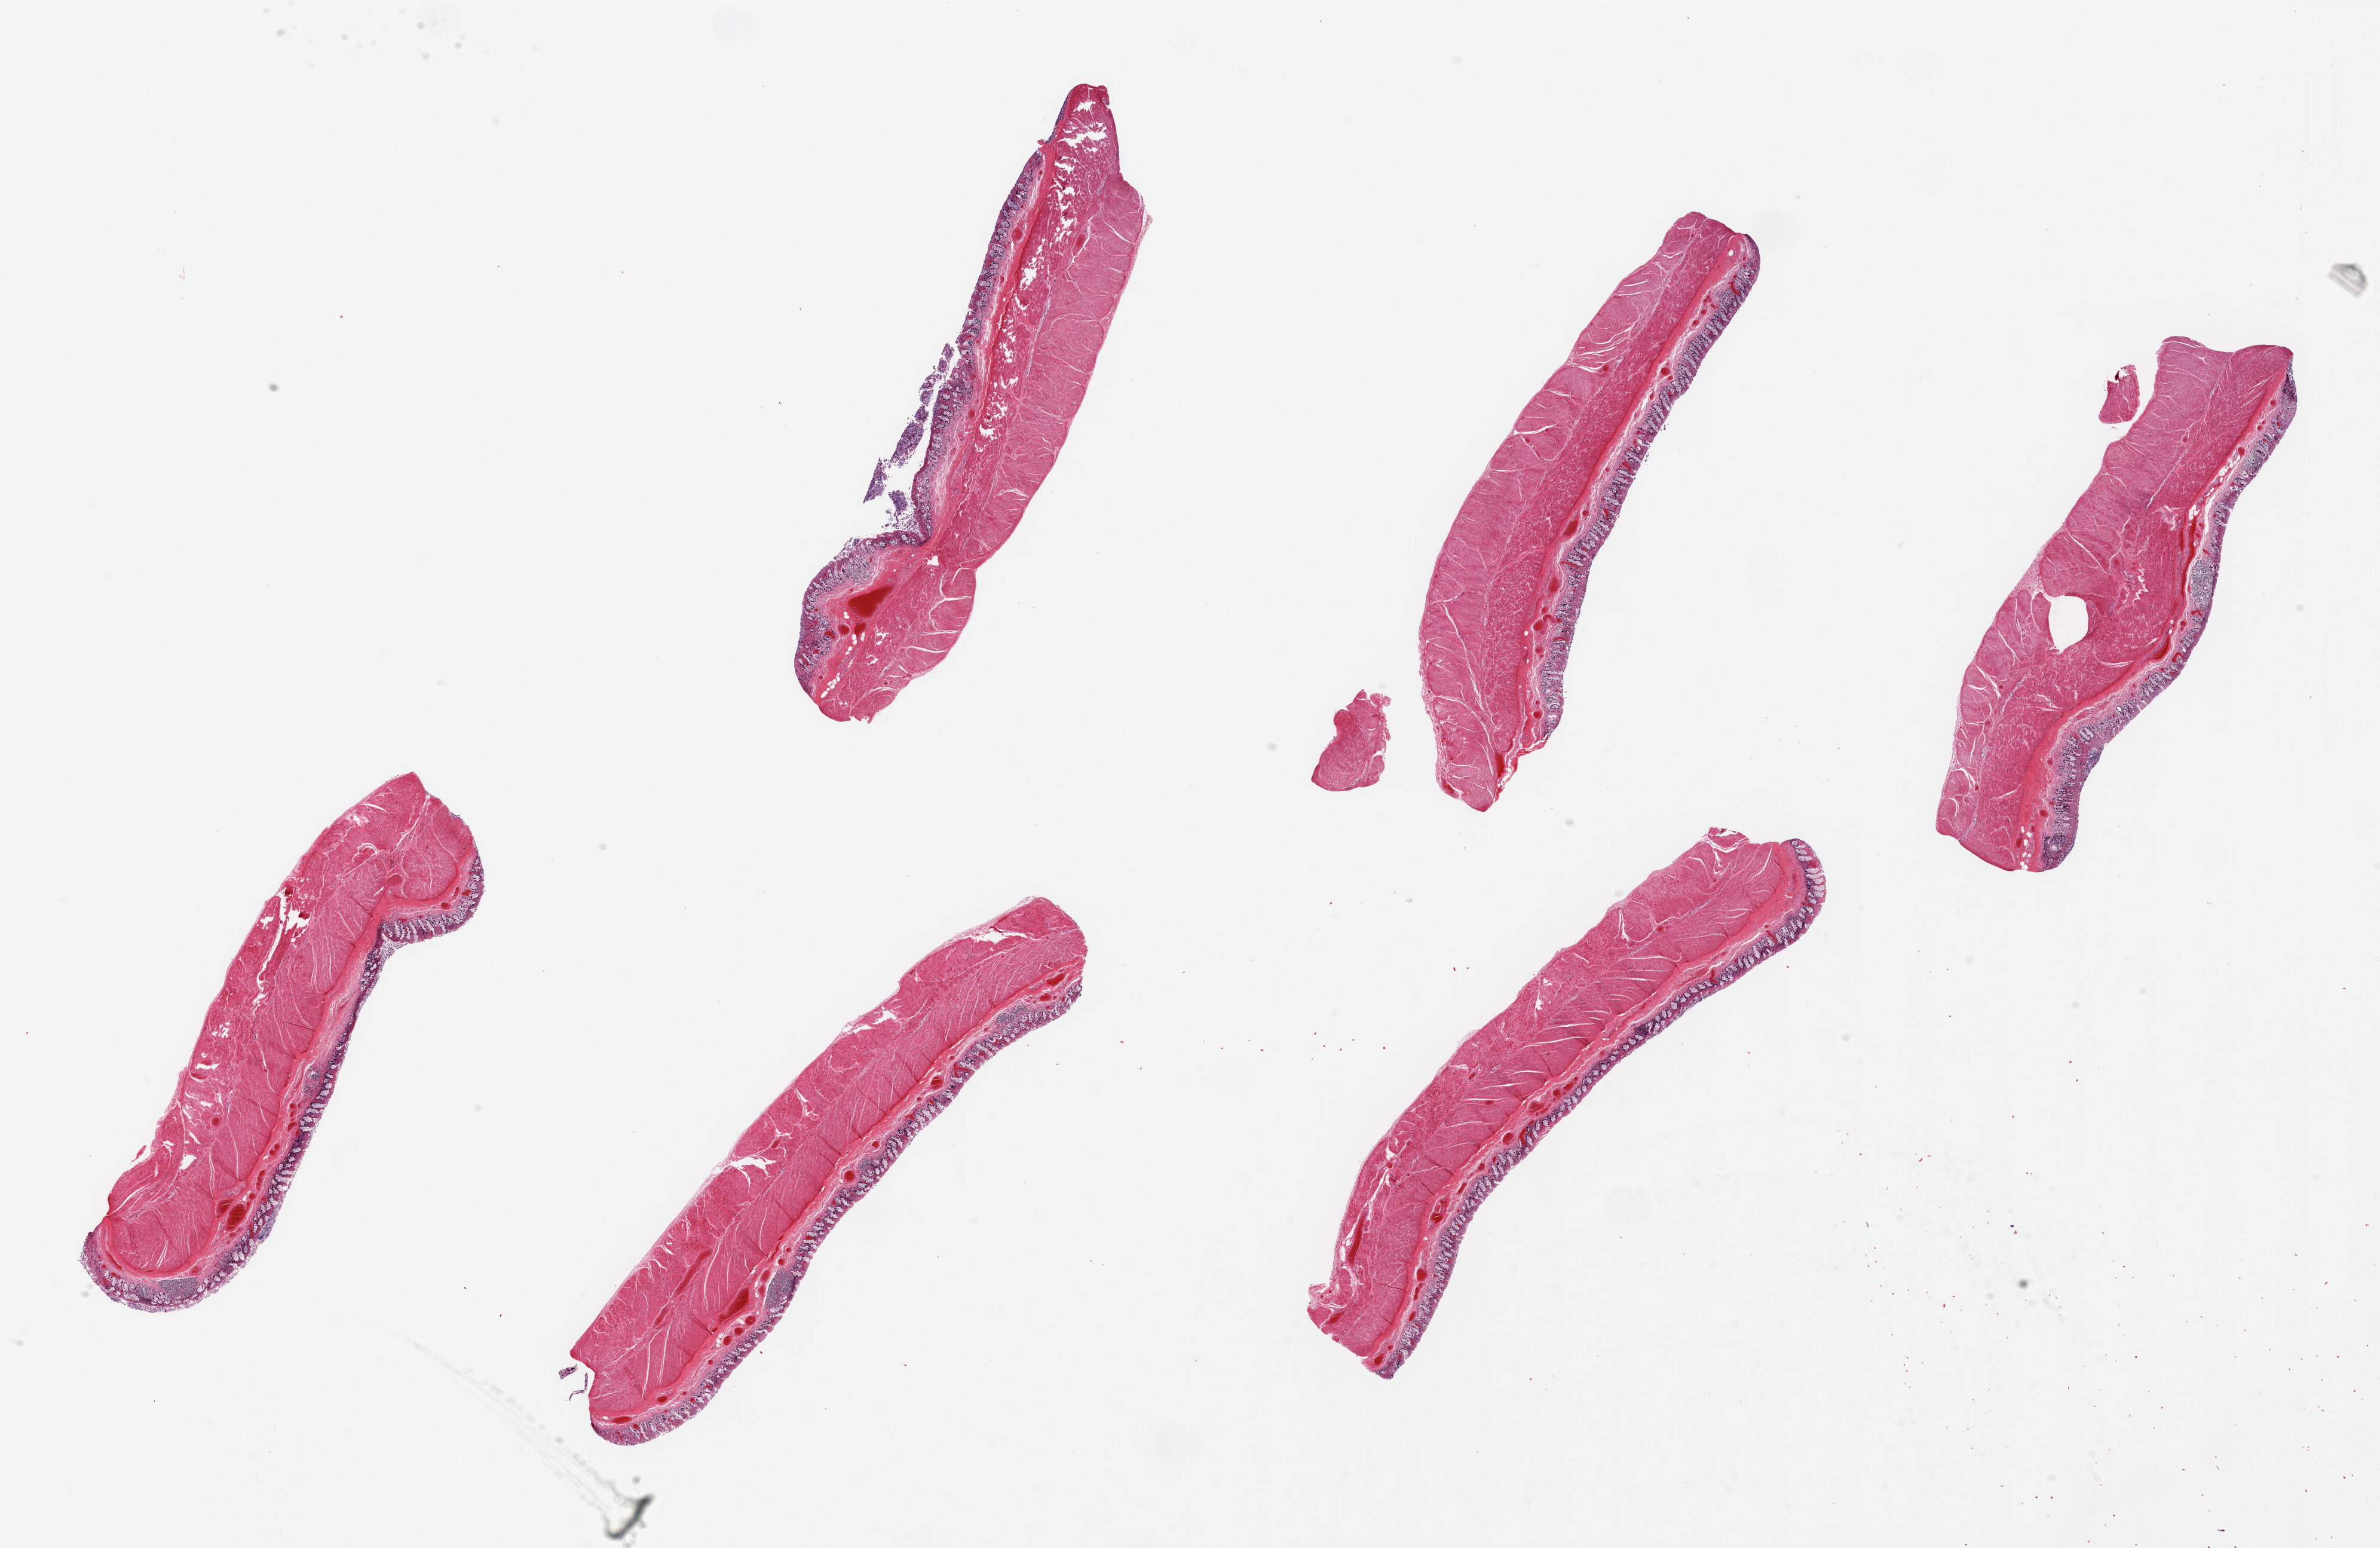
Whole-slide image, hematoxylin and eosin (H&E) stain — whole scanned area (about 31.5 x 20.5 mm, from a 20x scan) shown as a low-resolution overview; PAXgene-fixed, paraffin-embedded tissue; target tissue: sigmoid colon; donor tissue sample. Donor: female.
Pathologist's review note for this sample: 6 pieces ~8x2mm, 90% muscle, reprentative areas.